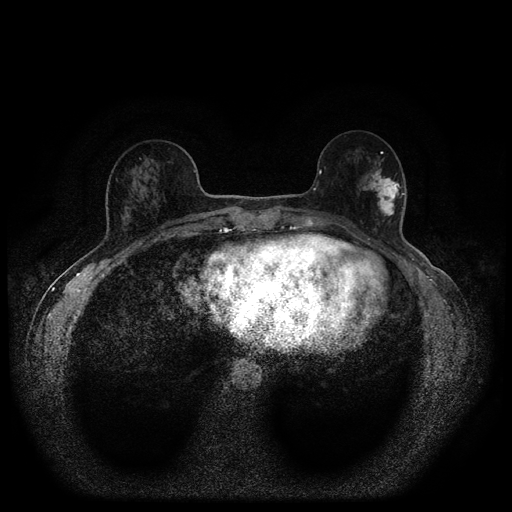
Breast MRI (dynamic contrast-enhanced, multi-phase), one axial slice; position 39 of 116 along the scan axis; dynamic contrast-enhanced series, time point 2 of 5 at this slice position (early post-contrast); 1.5 T; TE 2.7 ms, TR 5.4 ms; 2 mm slice thickness; 512 × 512 image matrix, field of view 330 × 330 mm. Patient: female, 56 years.
Structures marked on this image (semi-automatically segmented with operator editing):
- breast lesion (labelled 'tumour' in the annotation; benign lesions carry a separate 'benign' label): box from (x=360, y=159) to (x=404, y=221) px